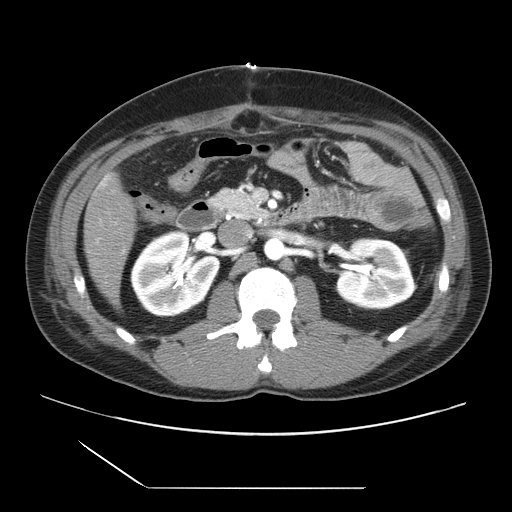
Contrast-enhanced abdominal CT, one axial slice. Slice 6 of 39 in the series (ordered by position). 120 kVp. Intravenous contrast given. Soft-tissue window (W 400 / L 40 HU). 5 mm slice thickness. 512 × 512 image matrix, field of view 395 × 395 mm. Male patient, age 39 years. Case-level facts recorded for this patient, not image findings: diagnosis: colorectal cancer liver metastases, imaged before liver resection; multiple liver metastases: yes; largest metastasis: 1.3 cm; disease in both lobes: no.
Annotated regions visible in this slice (manually delineated by an expert):
- liver: bounding box <85,176,136,302> (left, top, right, bottom; pixels)